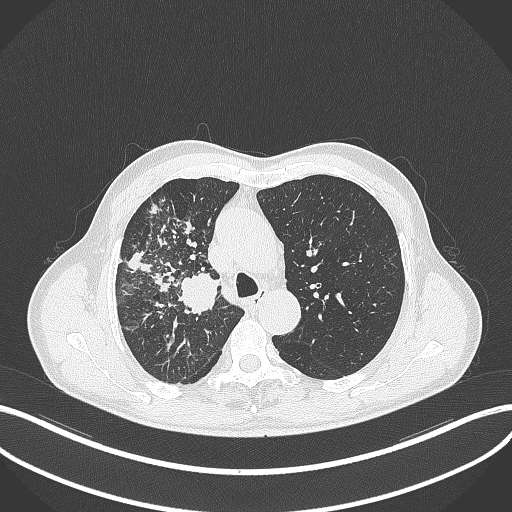
Chest CT, one axial slice. Slice 342 of 490 in the series (ordered by position). 120 kVp. Lung window (W 1500 / L -600 HU). 512 × 512 image matrix, field of view 400 × 400 mm. Male patient, age 69 years. From the clinical record (not read from this slice): clinical TNM (as recorded): T2a N0 M0.
Structures marked on this image (bounding box drawn by a radiologist):
- lung tumour (recorded histology: adenocarcinoma): bounding box <179,270,223,314> (left, top, right, bottom; pixels)